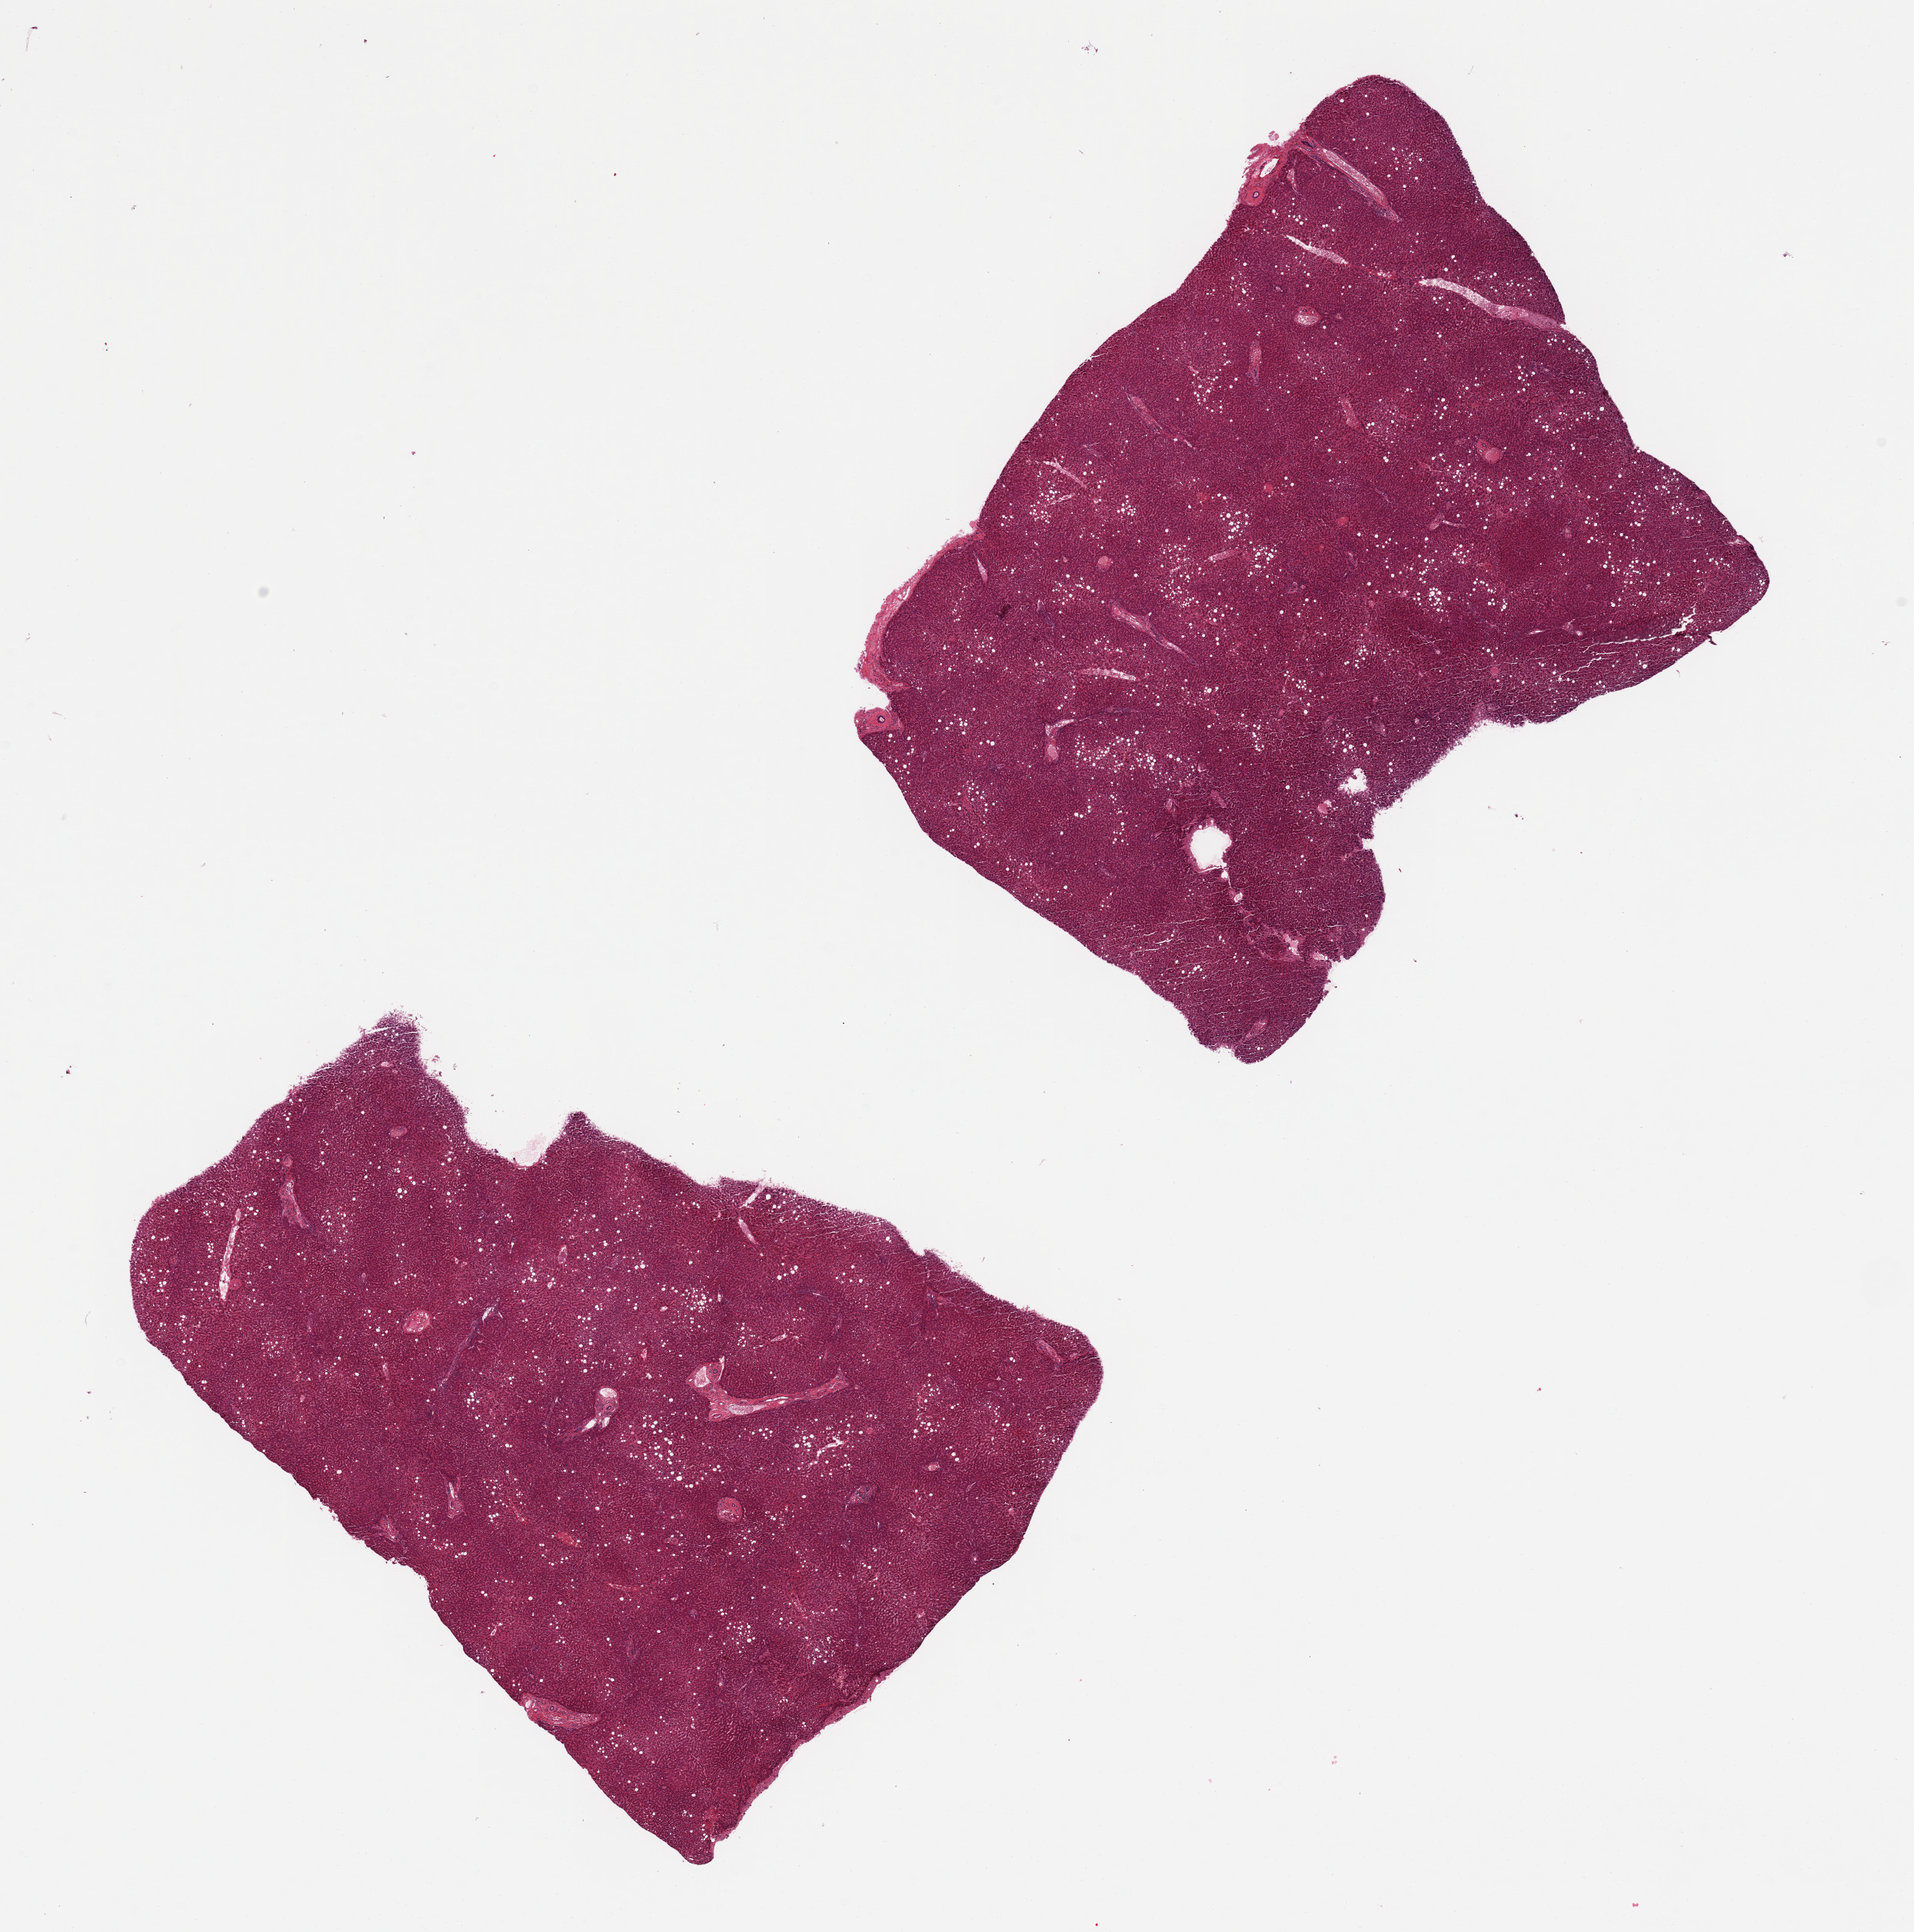
Haematoxylin and eosin whole-slide image — whole scanned area (about 19.7 x 19.9 mm) shown as a low-resolution overview; PAXgene-fixed paraffin-embedded (PFPE) section; target tissue: liver; donor tissue sample.
* review note (as recorded): 2 pieces. 10% macrovesicular steatosis